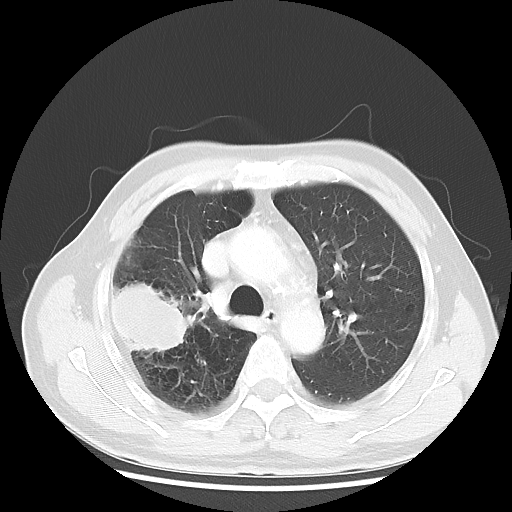
Chest CT, one axial slice. Position 35 of 50 along the scan axis. Reconstruction kernel LUNG. Lung window (W 1500 / L -600 HU). 512 × 512 image matrix. Patient: male, 69 years. Case-level facts recorded for this patient, not image findings: clinical TNM (as recorded): T3 N0 M0.
Structures marked on this image (bounding box drawn by a radiologist):
- lung tumour (recorded histology: adenocarcinoma): bounding box (x1, y1, x2, y2) in pixels: (111, 278, 194, 357)